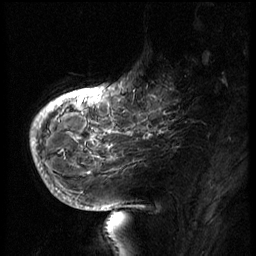
Breast MRI (dynamic contrast-enhanced), one sagittal slice; position 15 of 66 along the scan axis; 3 images stored at this slice position (order not interpretable as contrast timing); 1.5 T; TE 4.2 ms, TR 8.9 ms; 256 × 256 image matrix, field of view 200 × 200 mm. Patient: female, 56 years. Case-level facts recorded for this patient, not image findings: setting: breast cancer imaged before/during neoadjuvant chemotherapy.
Annotated regions visible in this slice (semi-automatically segmented with operator editing):
- analysis volume of interest (the breast-tissue region the enhancement analysis was run in; not a lesion): box from (x=129, y=62) to (x=194, y=127) px
- tumour enhancement mask (voxels above the 140 % enhancement threshold inside the analysis volume of interest): (x=141, y=89)–(x=175, y=127)